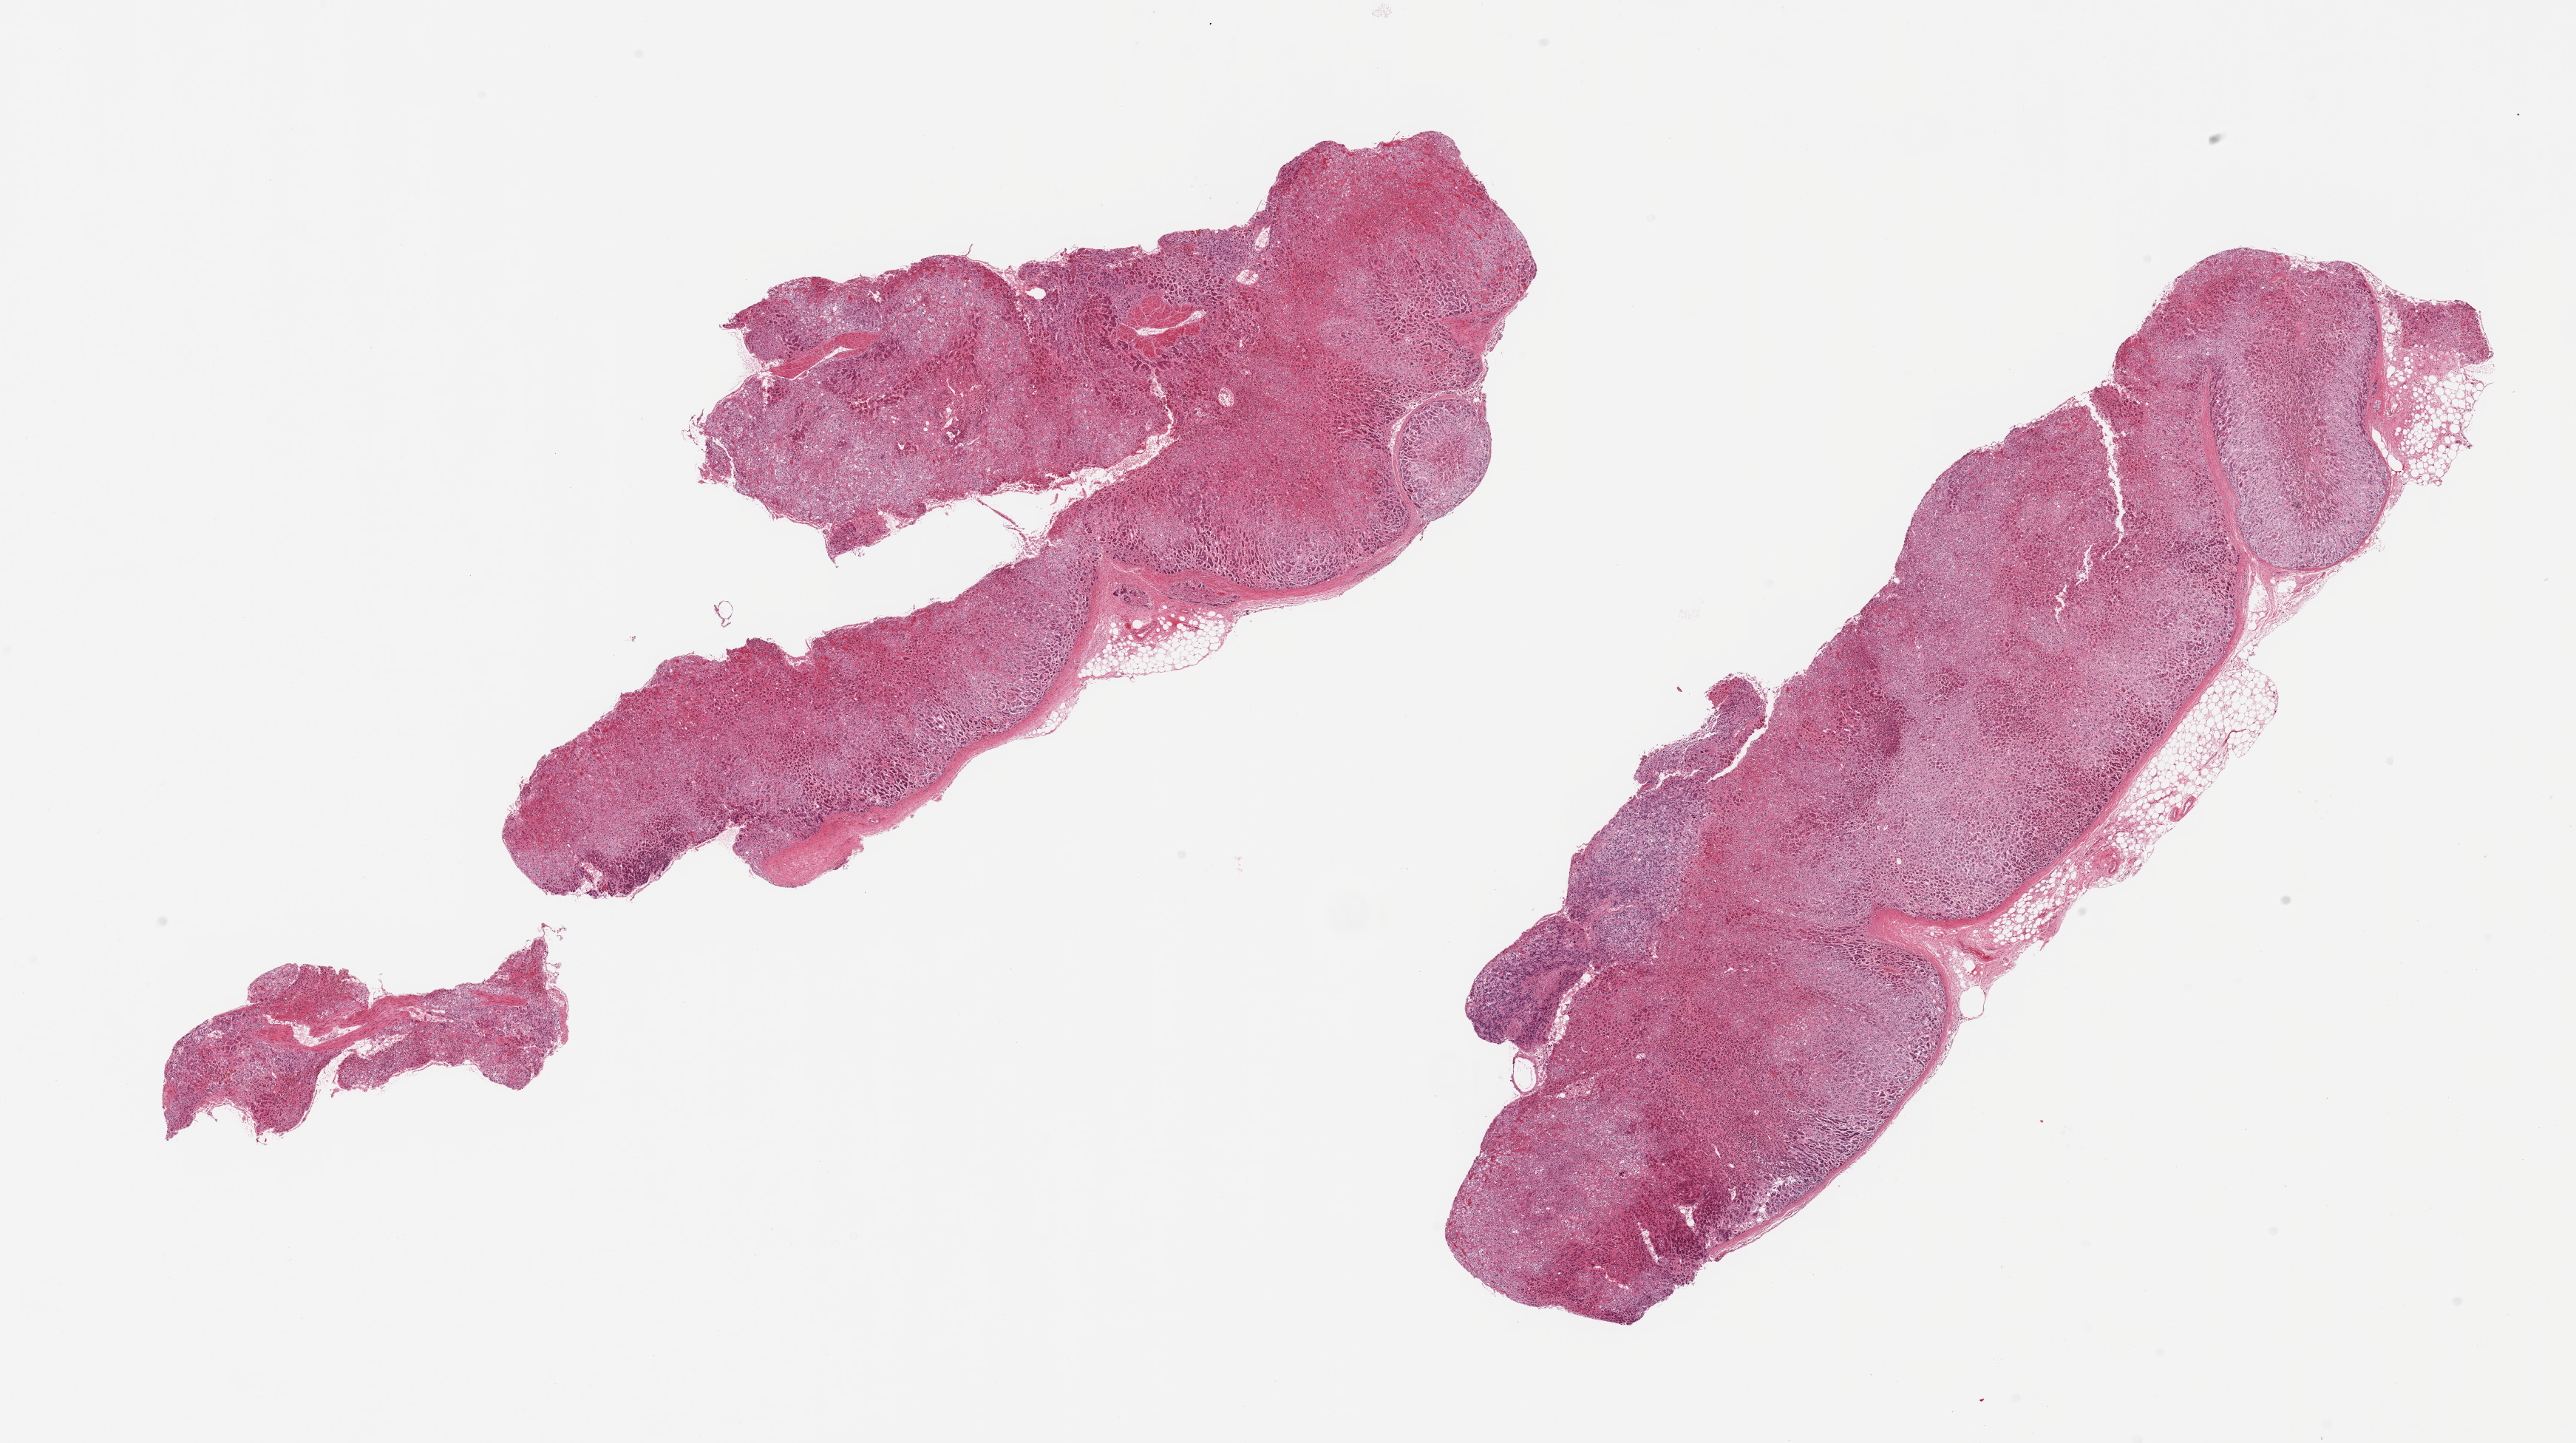
Digitized hematoxylin and eosin (H&E)-stained section, brightfield, shown as a low-resolution overview of the whole scanned area (about 27.6 x 15.4 mm, acquisition: 20x scan), PAXgene-fixed, paraffin-embedded tissue, target tissue: adrenal gland, donor tissue sample. Male donor.
Reviewer comment on this tissue sample: 2 pieces; cortex and medulla.